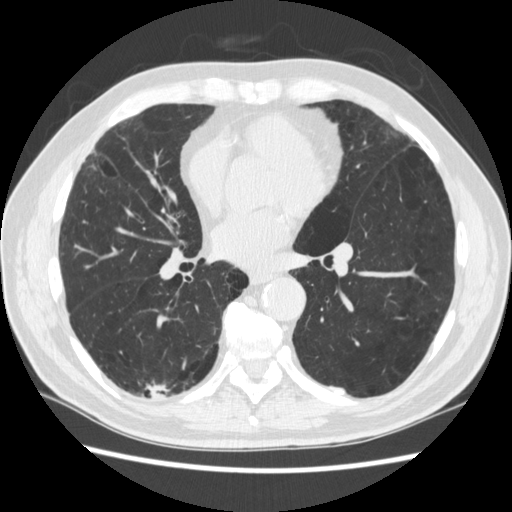
Low-dose screening chest CT, axial slice, third annual screen, lung window (W 1500 / L -600 HU), standard (soft-tissue) reconstruction kernel (STANDARD), slice 141 of 266 in the series. Male, age 70 years at enrolment. Former smoker at enrolment.
Expert reader's lesion annotation, bounding box [x1, y1, x2, y2] px = [121, 361, 186, 421]. The screening reader recorded 4 non-calcified nodules or masses ≥4 mm on this exam; which of them this box marks is not recorded. Official screen result: positive, other. Later outcome: lung cancer diagnosed 253 days after this screen — squamous cell carcinoma, NOS, right upper lobe, poorly differentiated (G3), stage IV (AJCC 6th edition).